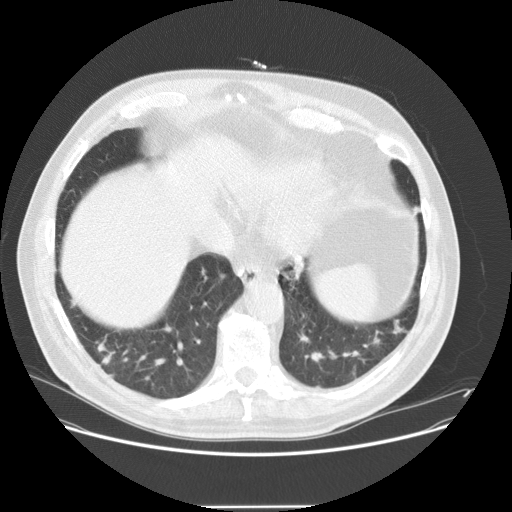
Chest CT (low-dose screening protocol), one axial image, first (baseline) screen, lung window (W 1500 / L -600 HU), 120 kVp, slice 100 of 143 in the series, 512 × 512 image matrix. Male participant, aged 61 years at enrolment. Current smoker at enrolment.
Expert-annotated lung lesion, bounding box [x1, y1, x2, y2] px = [88, 328, 141, 381]. The screening reader recorded 2 non-calcified nodules or masses ≥4 mm on this exam (left lower lobe, right lower lobe); which of them this box marks is not recorded. Official screen result: positive, change unspecified: nodule(s) >= 4 mm or enlarging nodule(s), mass(es), or other non-specific abnormalities suspicious for lung cancer.